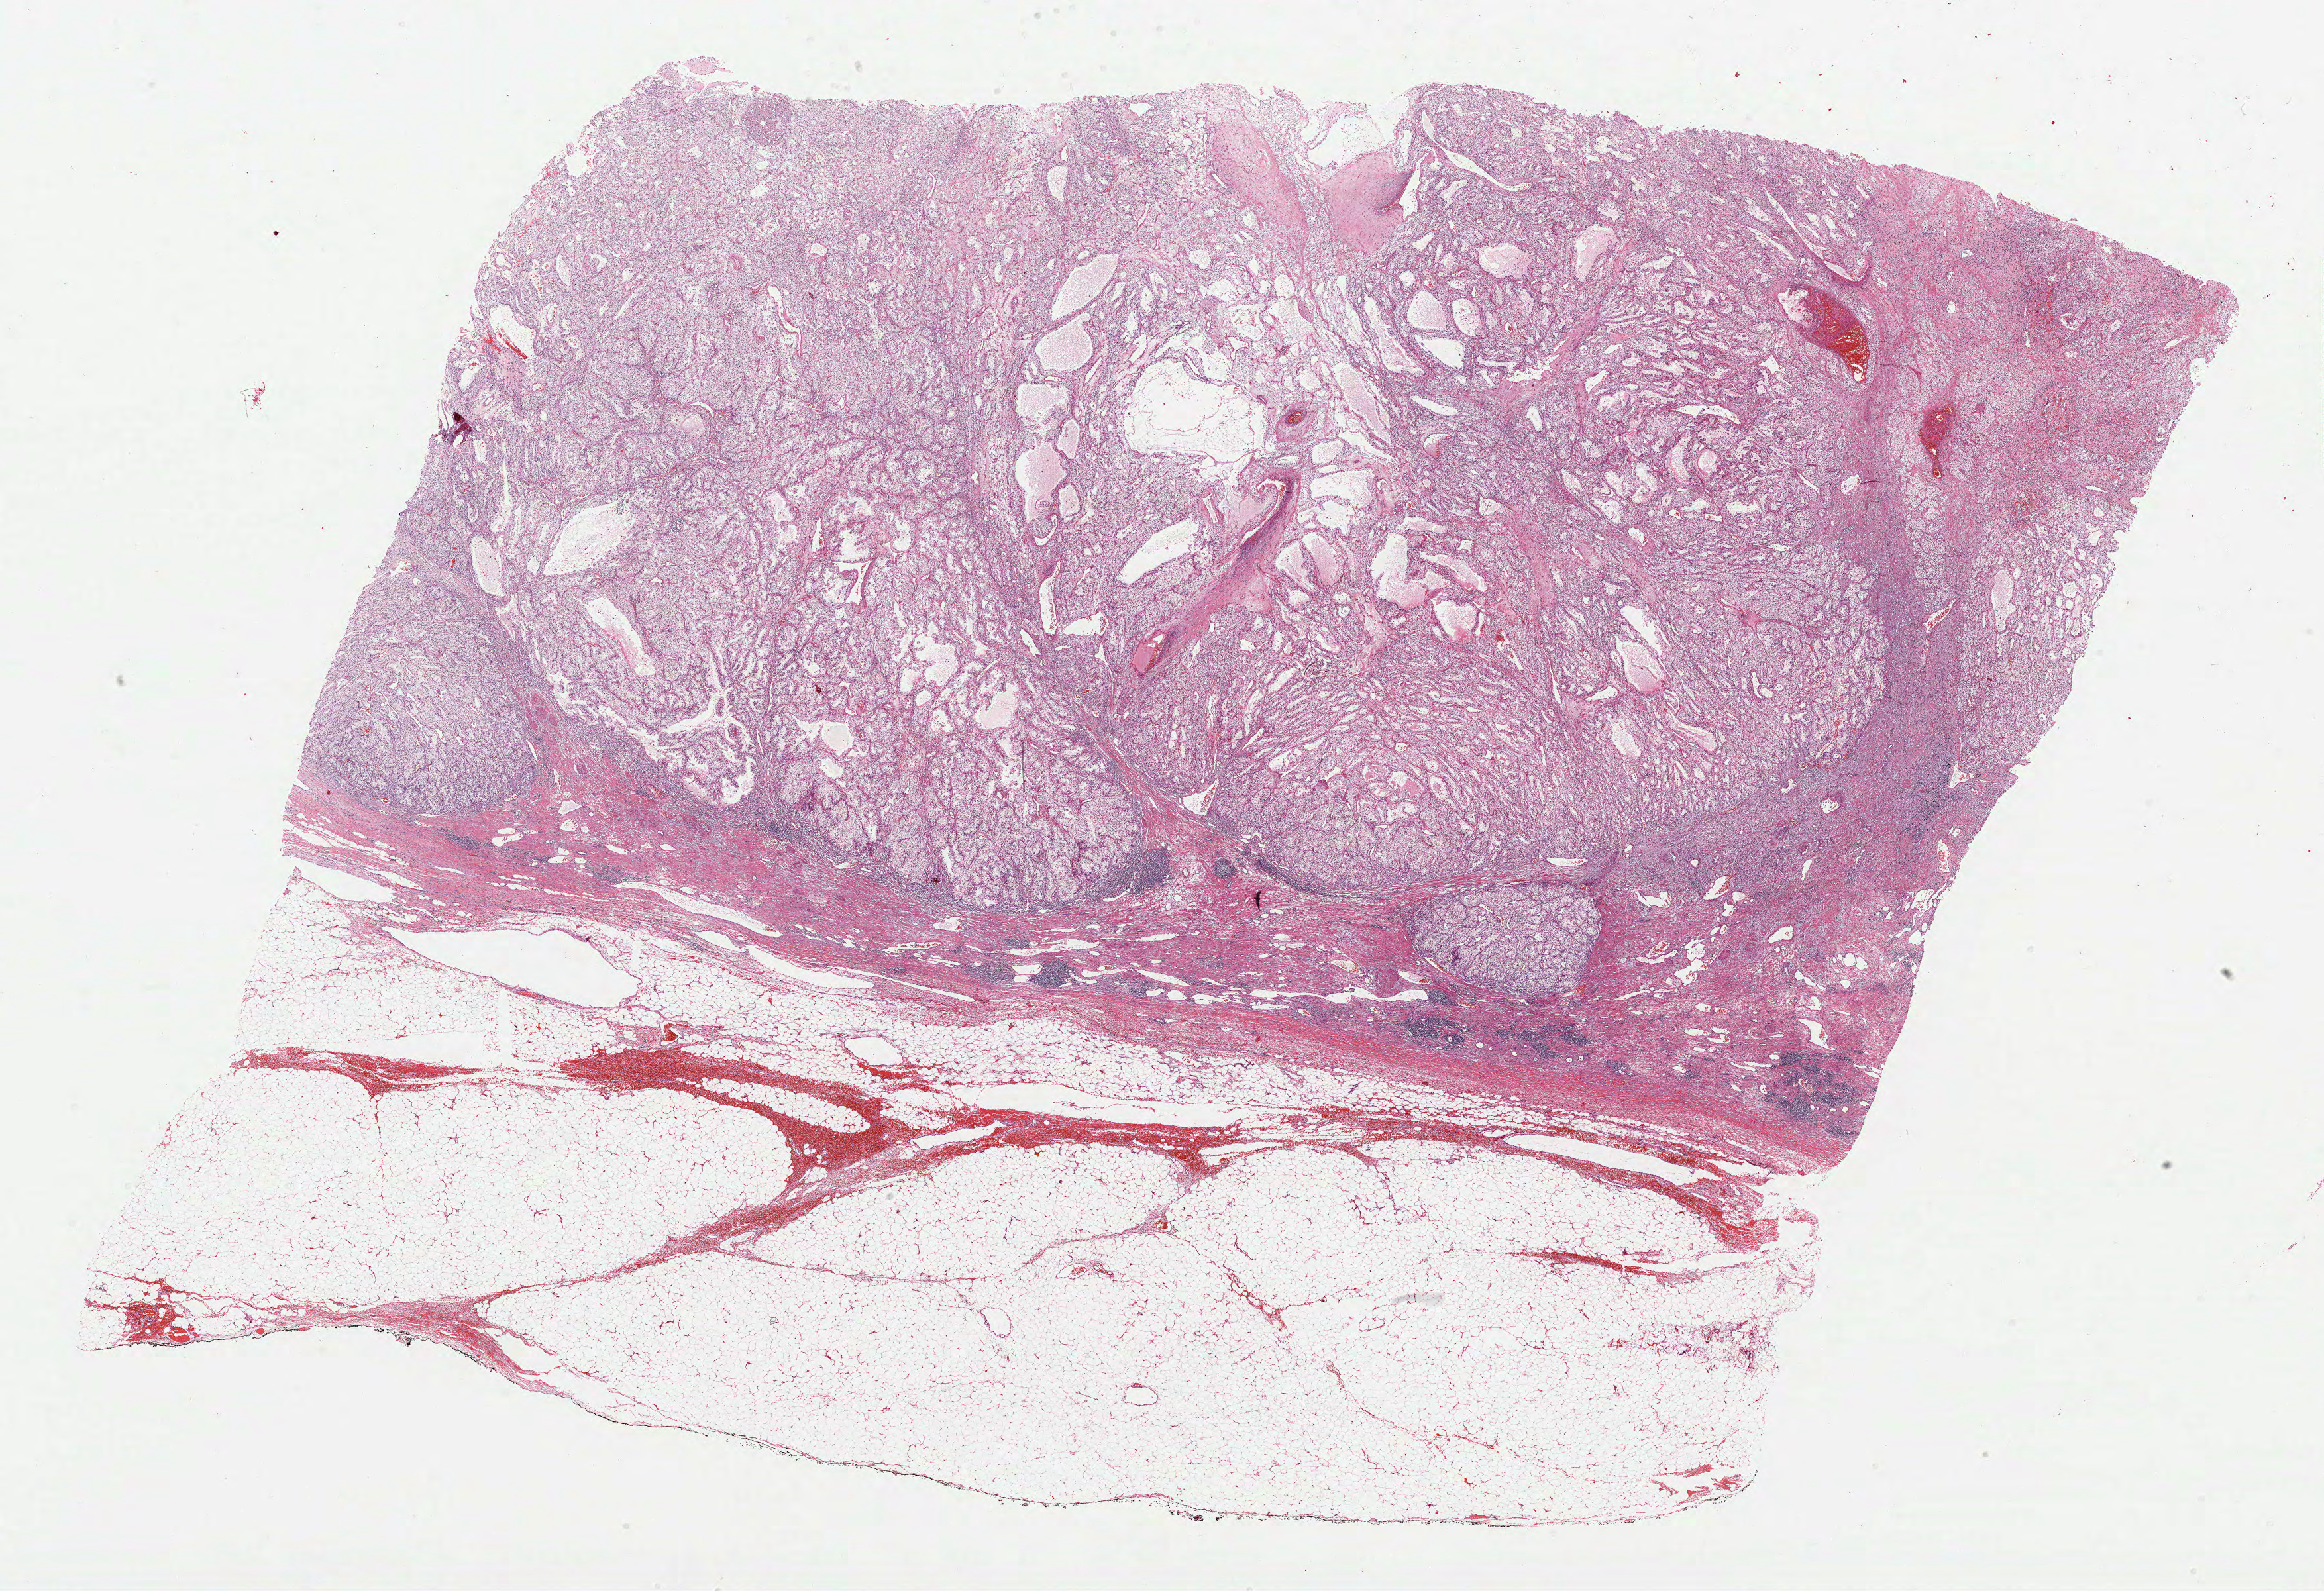
Digitized Hematoxylin and eosin (H&E) stained tissue section (whole slide), low-resolution overview of the scanned area, about 28.3 x 19.4 mm (from a 40x scan). Formalin-fixed paraffin-embedded (FFPE) diagnostic section. Primary tumour sample from the kidney. Patient: male, age at initial diagnosis 63 years. Histologic grade: G2 (moderately differentiated).
* lymph nodes positive (case pathology): 0 of 3 examined
* TNM: T2 N0 M1
* AJCC pathologic stage: IV
* laterality: right
* diagnosis: Clear cell adenocarcinoma, NOS